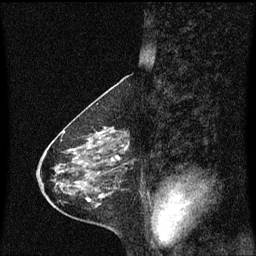
Breast MRI (dynamic contrast-enhanced), one sagittal slice. Dynamic contrast-enhanced series, image 2 of 3 at this slice position (ordered by acquisition). 1.5 T. TE 4.2 ms, TR 8.4 ms. 2 mm slice thickness. 256 × 256 image matrix, field of view 200 × 200 mm. Female patient, age 58 years.
Outlined on this slice (semi-automatic segmentation, software-assisted and operator-edited):
- analysis volume of interest (the breast-tissue region the enhancement analysis was run in; not a lesion): box from (x=100, y=127) to (x=129, y=160) px
- tumour enhancement mask (voxels above the 70 % enhancement threshold inside the analysis volume of interest): (x=100, y=127)–(x=129, y=160)